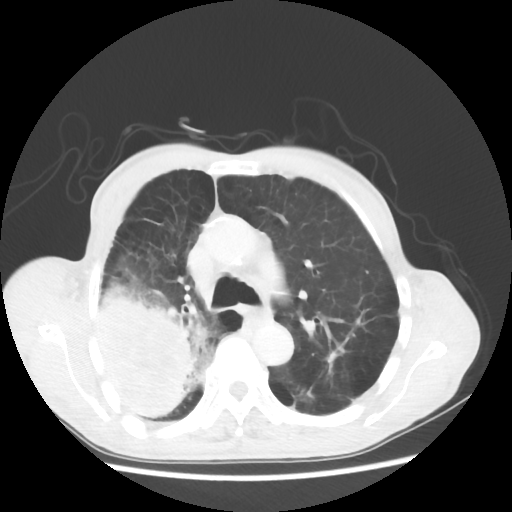
Chest CT, one axial slice; slice 36 of 58 in the series (ordered by position); reconstruction kernel STANDARD; lung window (W 1500 / L -600 HU); 5 mm slice thickness; 512 × 512 image matrix, field of view 351 × 351 mm. Patient: male, 75 years. Case-level facts recorded for this patient, not image findings: clinical TNM (as recorded): T4 N1 M1.
Structures marked on this image (bounding box drawn by a radiologist):
- lung tumour (recorded histology: adenocarcinoma): box from (x=93, y=274) to (x=211, y=418) px